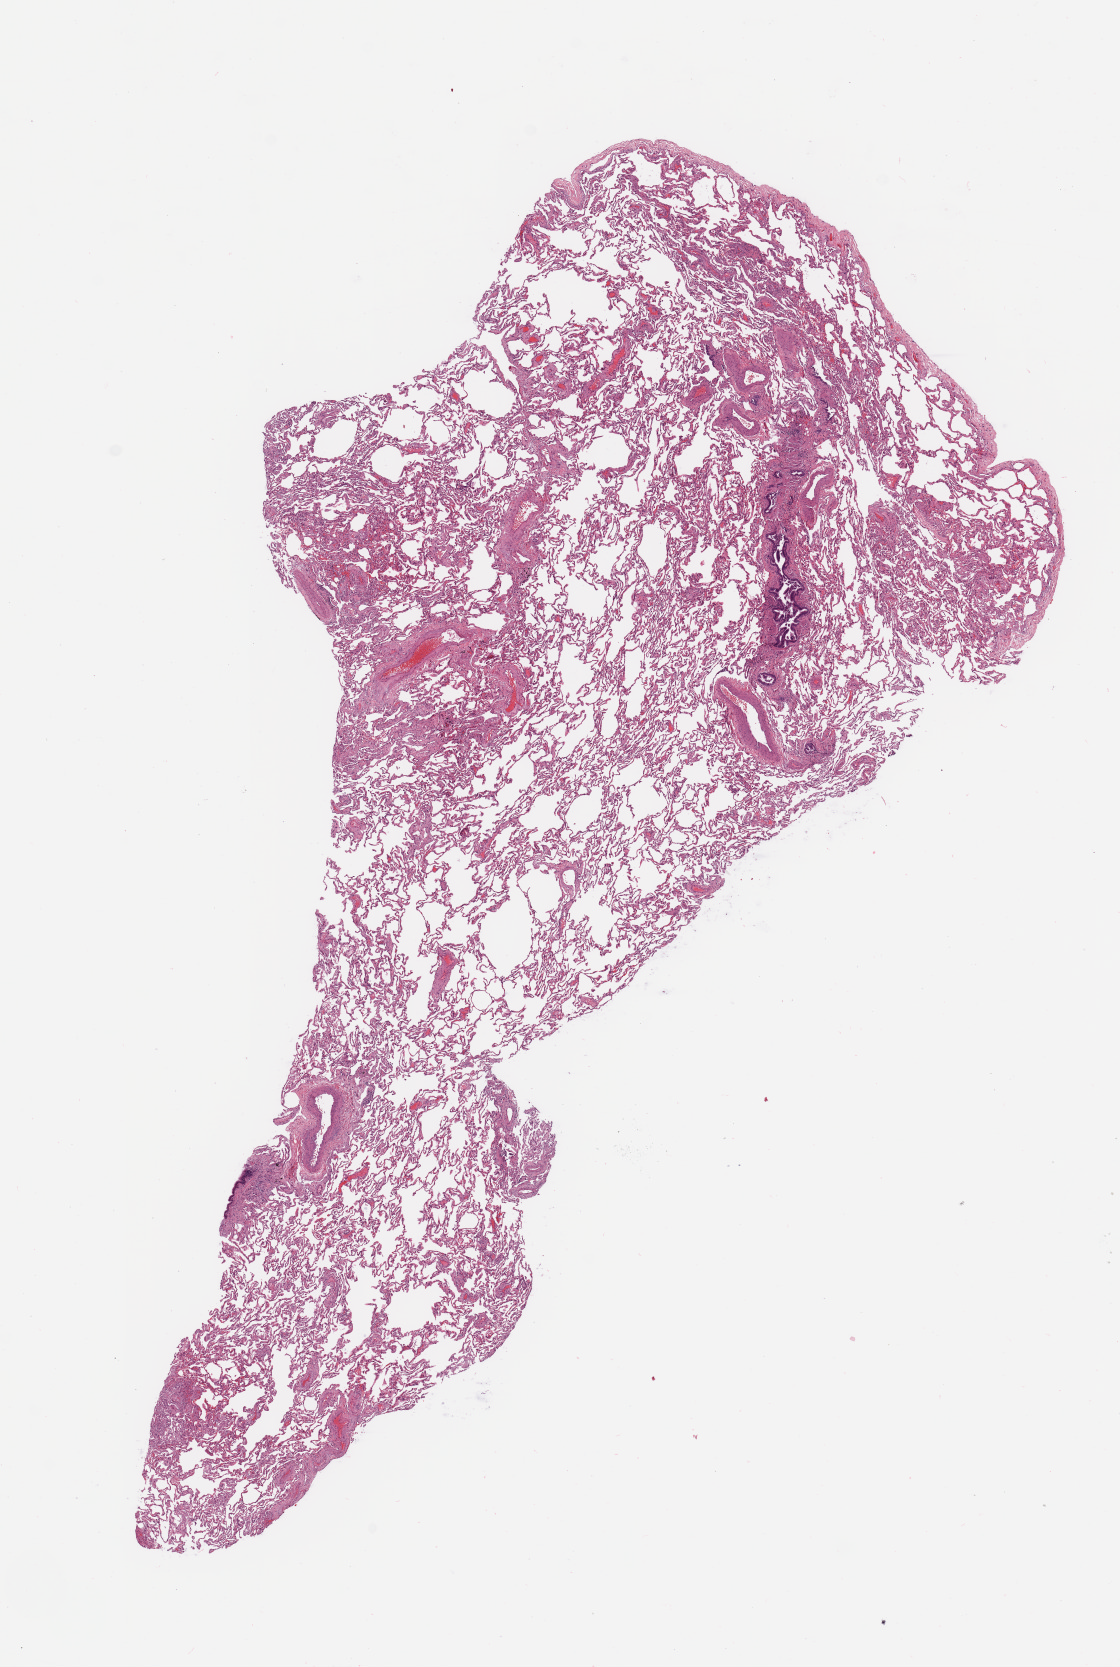
H&E-stained whole-slide image, whole scanned area (about 8.9 x 13.2 mm, from a 20x scan) shown as a low-resolution overview, lung, normal (non-tumour) tissue. 68-year-old female patient.
- this section: normal (non-tumour) tissue from the same patient
- patient diagnosis: Adenocarcinoma, NOS